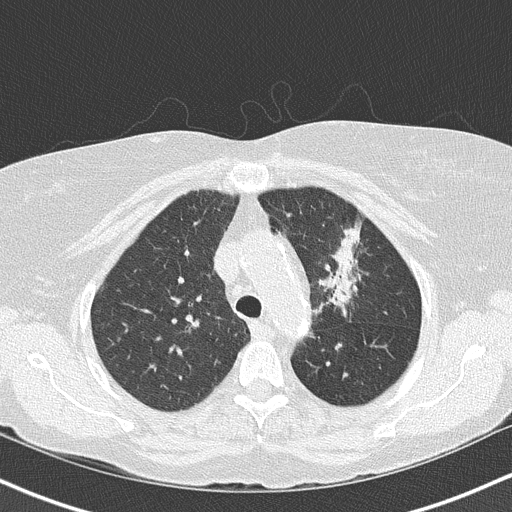
Low-dose screening chest CT, one axial slice. Position 112 of 147 along the scan axis. Reconstruction kernel B50f. Lung window (W 1500 / L -600 HU). 512 × 512 image matrix, field of view 320 × 320 mm.
Annotated regions visible in this slice (manually delineated by an expert):
- lesion 1 (tumor, upper lobe of left lung): bounding box [x1, y1, x2, y2] px = [332, 226, 359, 306]